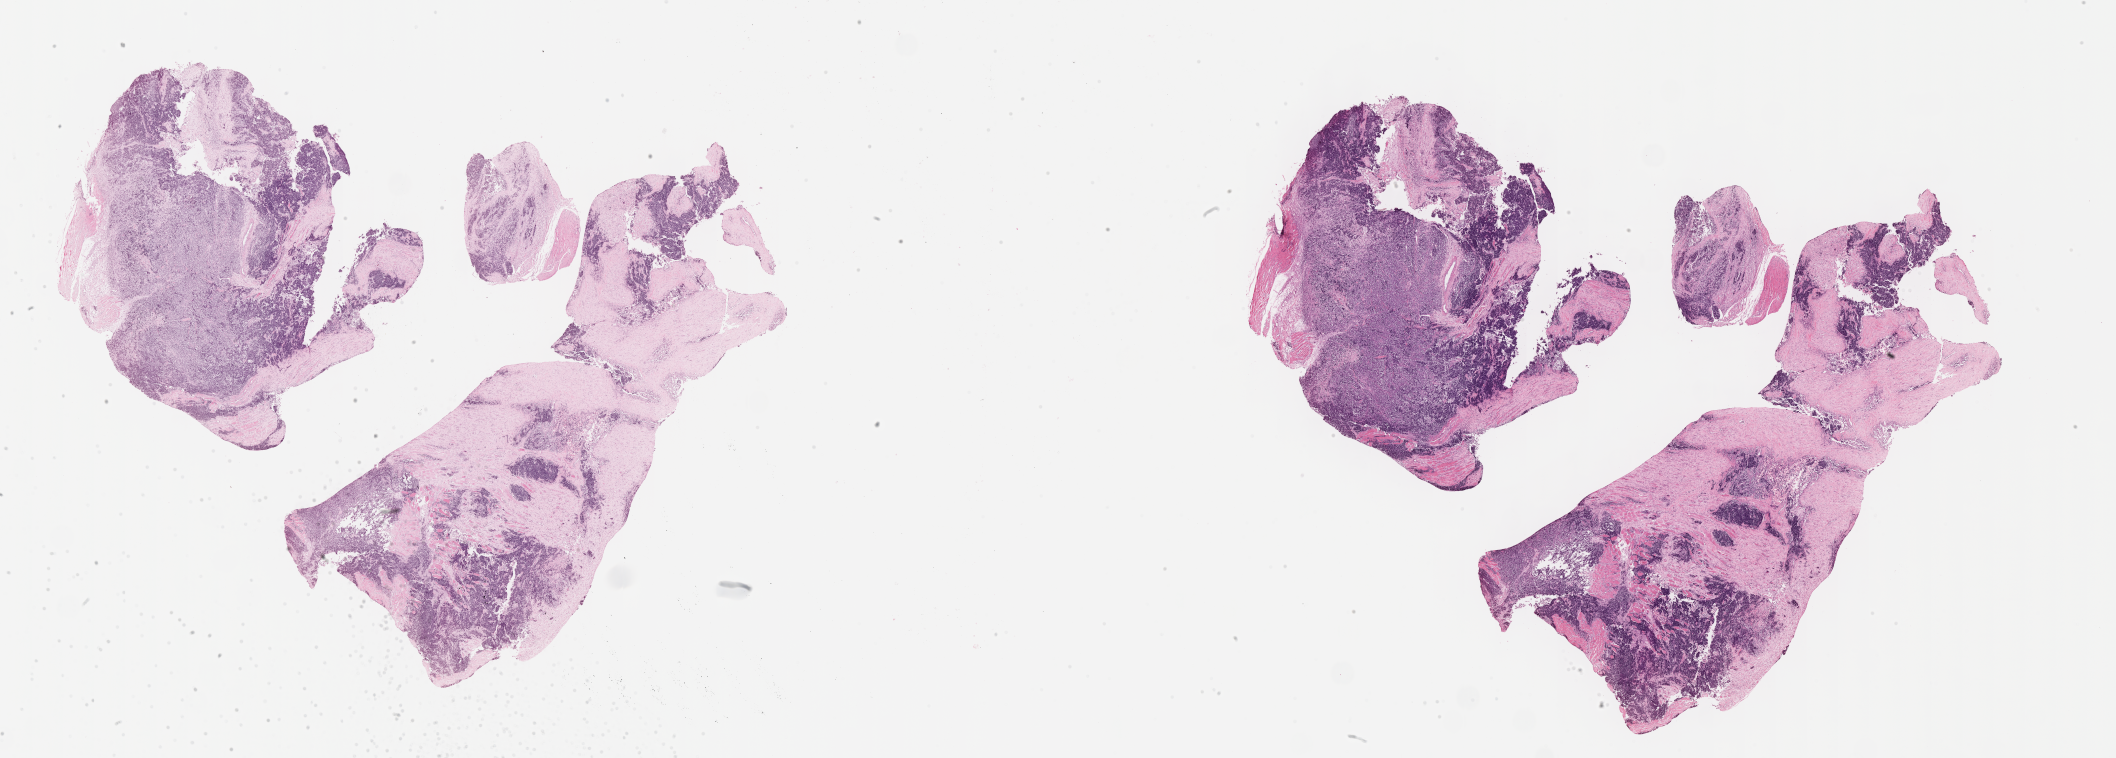
Hematoxylin and eosin (H&E) whole-slide image of tumor tissue — shown as a low-resolution overview of the whole scanned area (about 34.2 x 12.3 mm), FFPE section, site: soft tissue, forearm. Female patient, age at diagnosis 15.2 years.
- metastatic status at presentation (as recorded): non-metastatic (unconfirmed)
- stage (as recorded): 3
- diagnosis: rhabdomyosarcoma; histological classification: alveolar rhabdomyosarcoma